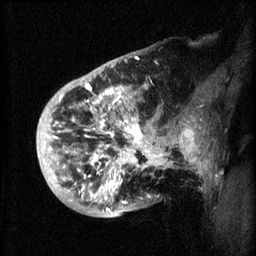
Breast MRI (dynamic contrast-enhanced), one sagittal slice; position 14 of 60 along the scan axis; 3 images stored at this slice position (order not interpretable as contrast timing); 1.5 T; TE 4.2 ms, TR 8.2 ms; 256 × 256 image matrix. Female patient, age 50 years.
Outlined on this slice (semi-automatic segmentation, software-assisted and operator-edited):
- analysis volume of interest (the breast-tissue region the enhancement analysis was run in; not a lesion): box from (x=44, y=72) to (x=173, y=219) px
- tumour enhancement mask (voxels above the 70 % enhancement threshold inside the analysis volume of interest): (x=60, y=84)–(x=168, y=213)